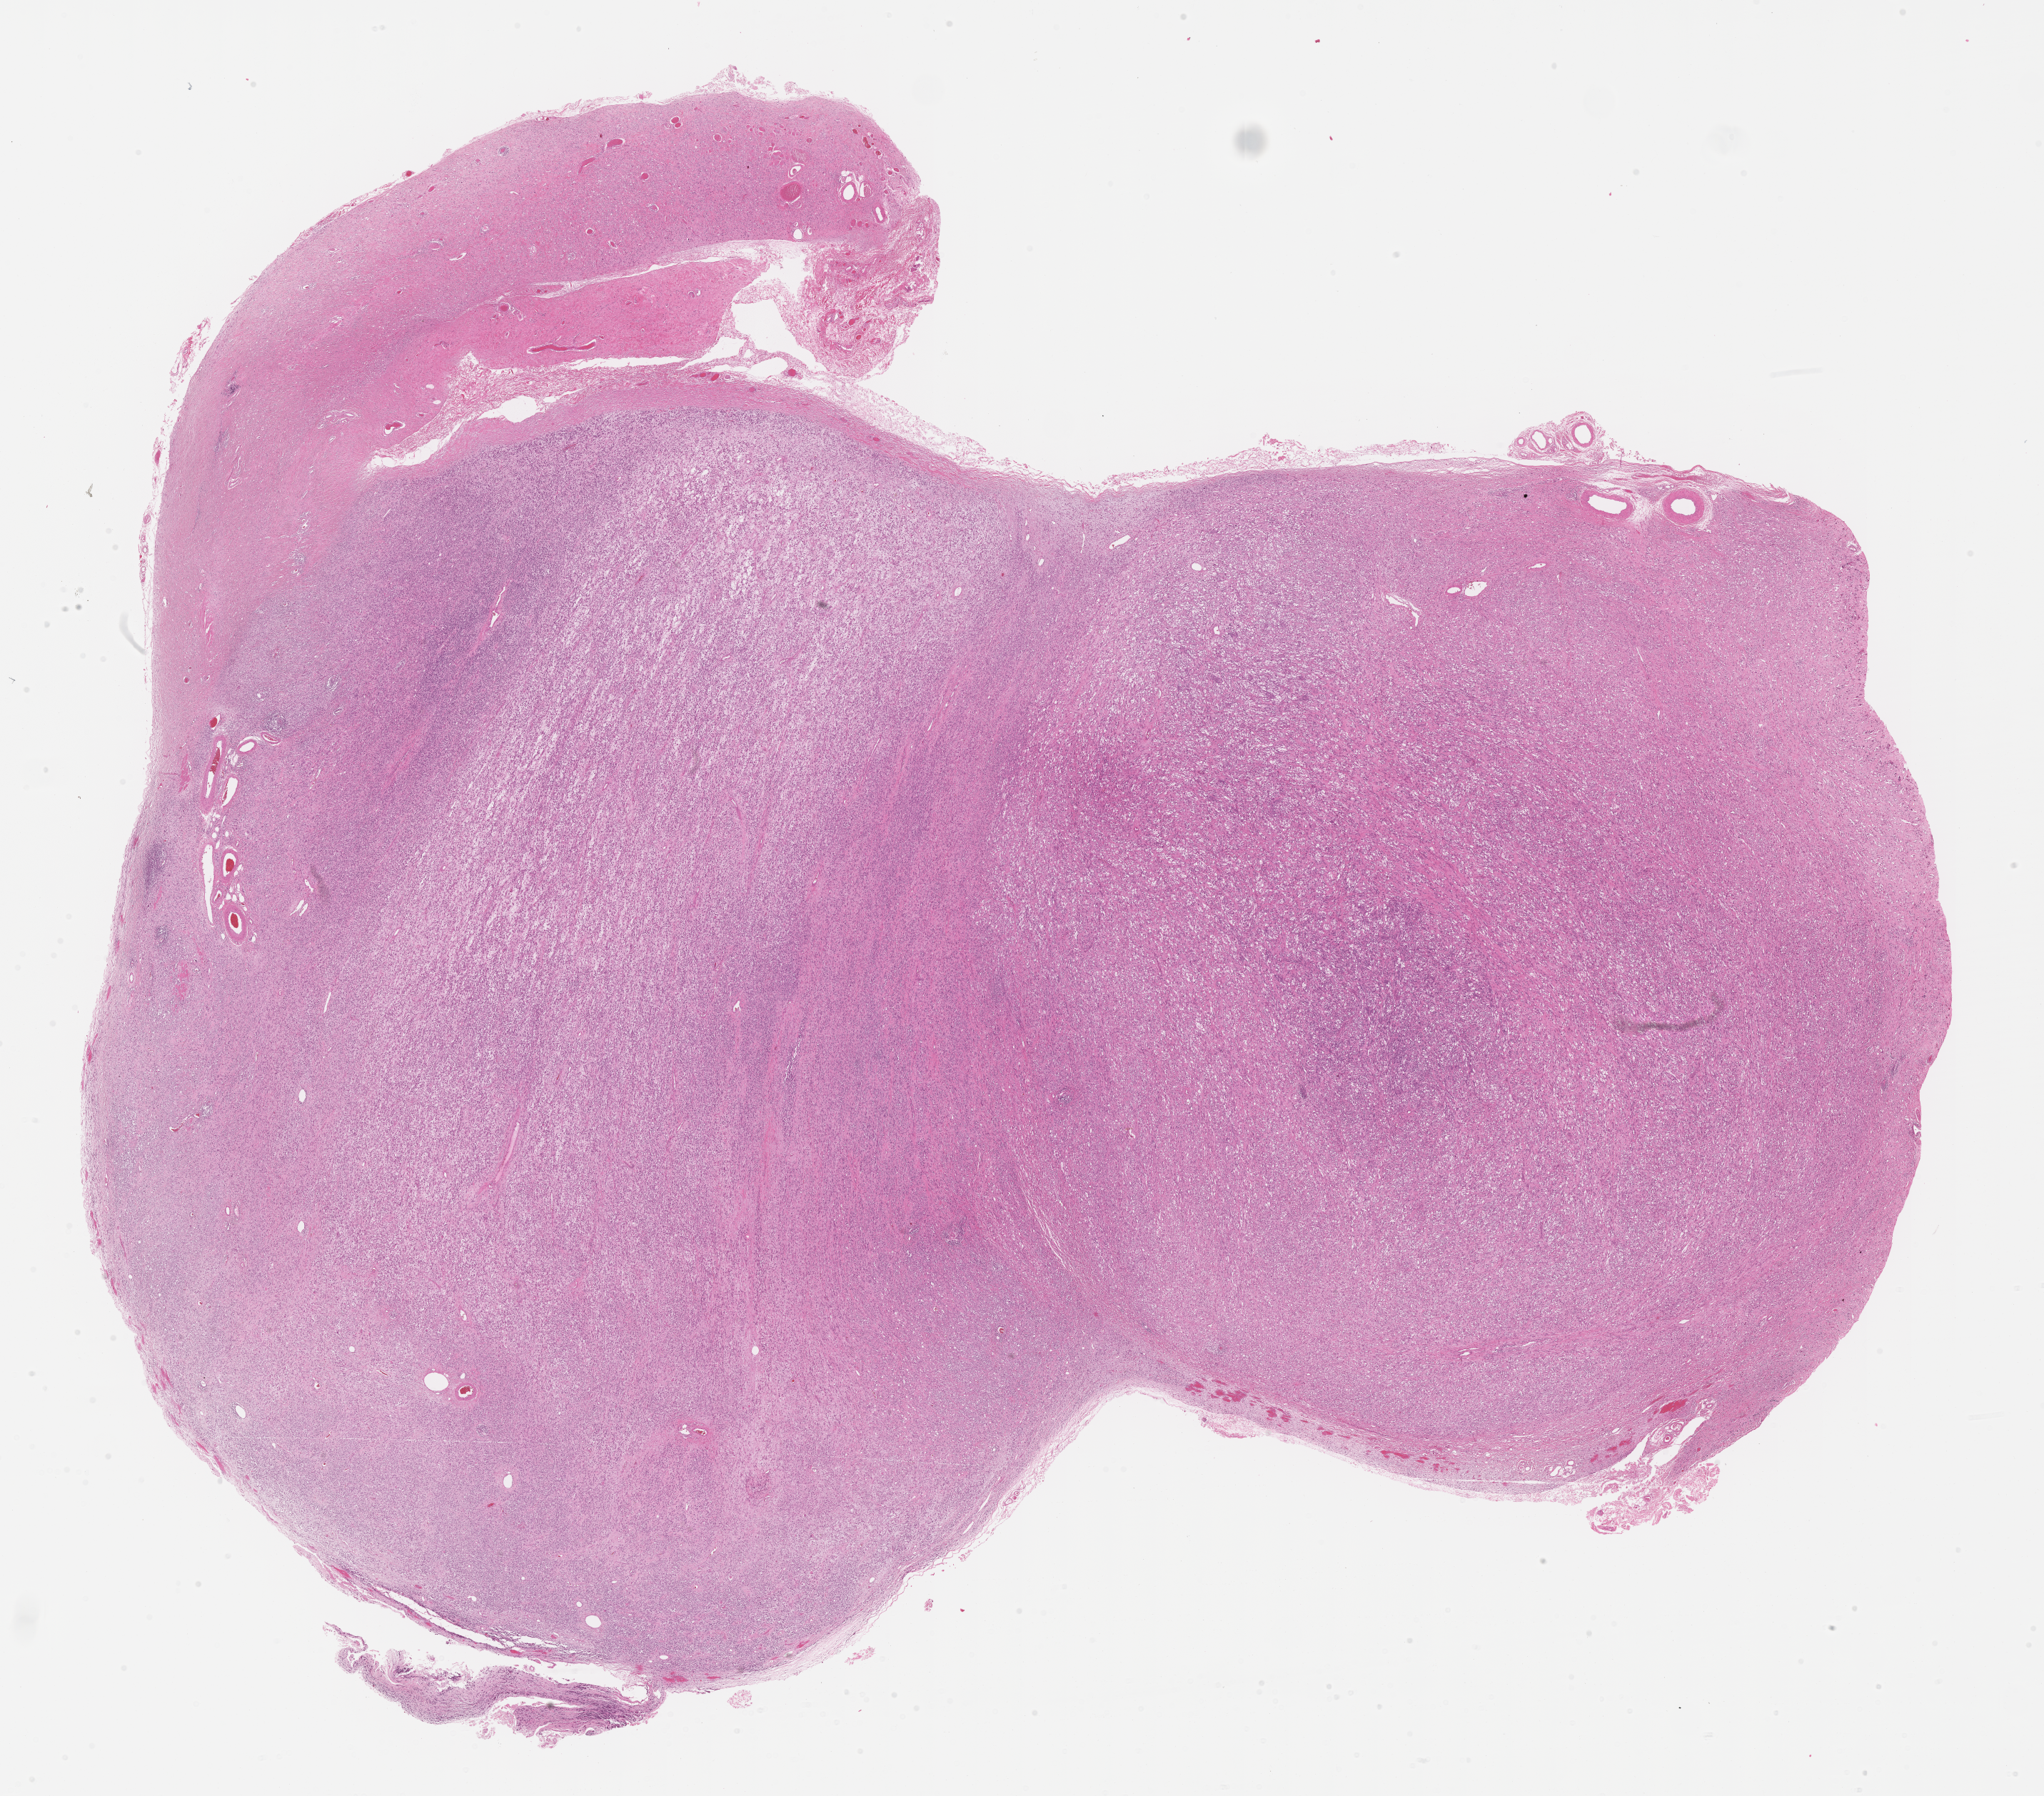
Digitized hematoxylin and eosin (H&E)-stained section of tumor tissue — low-resolution overview of the scanned area, about 23.1 x 20.3 mm. Formalin-fixed paraffin-embedded section. Sample anatomic site: testicle, left. Male patient, age at diagnosis 17.7 years.
- primary site (case record): testis-paratesticular
- stage (as recorded): 1
- metastatic status at presentation (as recorded): non-metastatic (confirmed)
- diagnosis: rhabdomyosarcoma; histological classification: spindle cell rhabdomyosarcoma